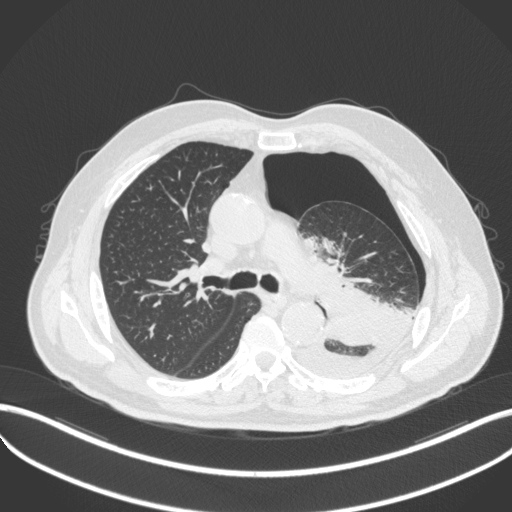
Chest CT, one axial slice. Position 330 of 466 along the scan axis. 120 kVp. Lung window (W 1500 / L -600 HU). 1 mm slice thickness. 512 × 512 image matrix. Patient: male, 76 years. Case-level facts recorded for this patient, not image findings: clinical TNM (as recorded): T3 N0 M1b.
Annotated regions visible in this slice (bounding box drawn by a radiologist):
- lung tumour (recorded histology: adenocarcinoma): bounding box (x1, y1, x2, y2) in pixels: (315, 282, 404, 349)